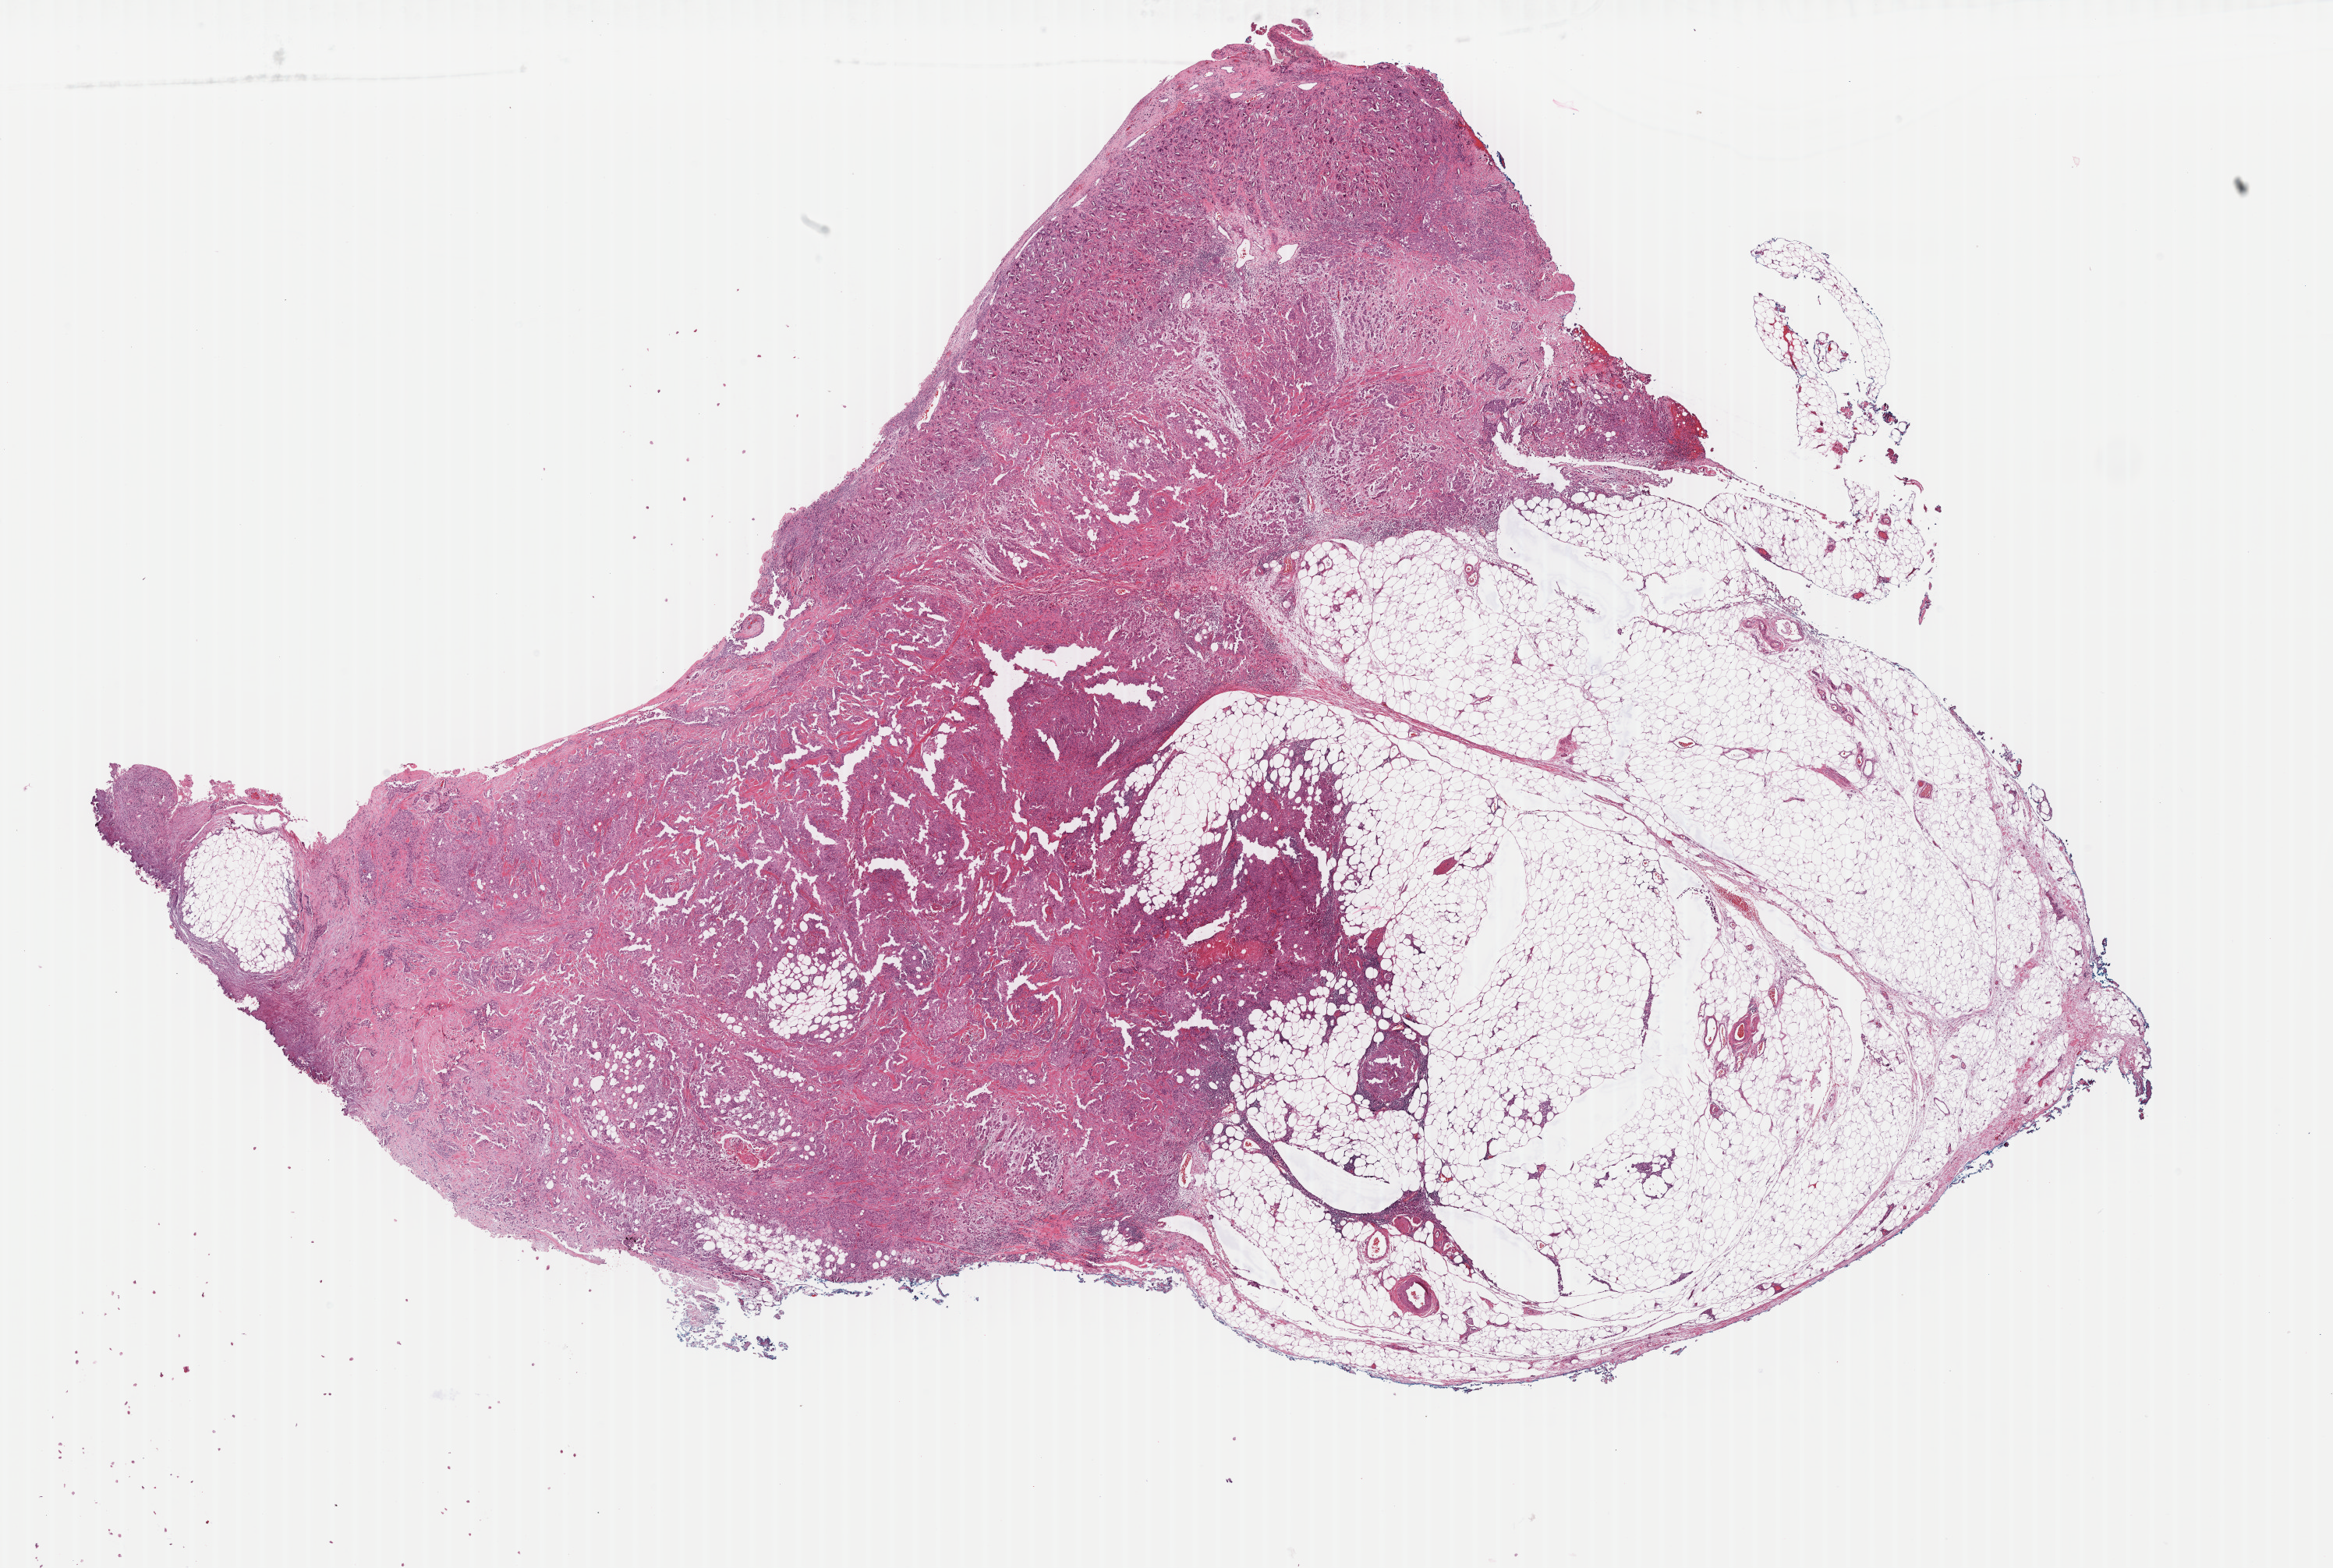
H&E-stained whole-slide image — whole scanned area (about 23.8 x 16.0 mm, slide scanned at 40x) shown as a low-resolution overview, formalin-fixed paraffin-embedded (FFPE) diagnostic section, sample: primary tumour, mesothelium. Female patient; age at initial diagnosis 68 years.
• pathologic diagnosis: Epithelioid mesothelioma, malignant (pleura, NOS)
• TNM: T3 N0 M0
• AJCC pathologic stage: III (7th edition)
• laterality: right